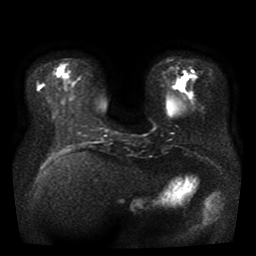
Breast MRI, one axial slice. Position 12 of 41 along the scan axis. Diffusion-weighted series; image 2 of 4 stored at this slice position (different b-values; order by instance number). 1.5 T. 256 × 256 image matrix, field of view 330 × 330 mm. Female patient.
Outlined on this slice (manually delineated by an expert):
- tumour on diffusion-weighted imaging: box from (x=192, y=74) to (x=197, y=78) px